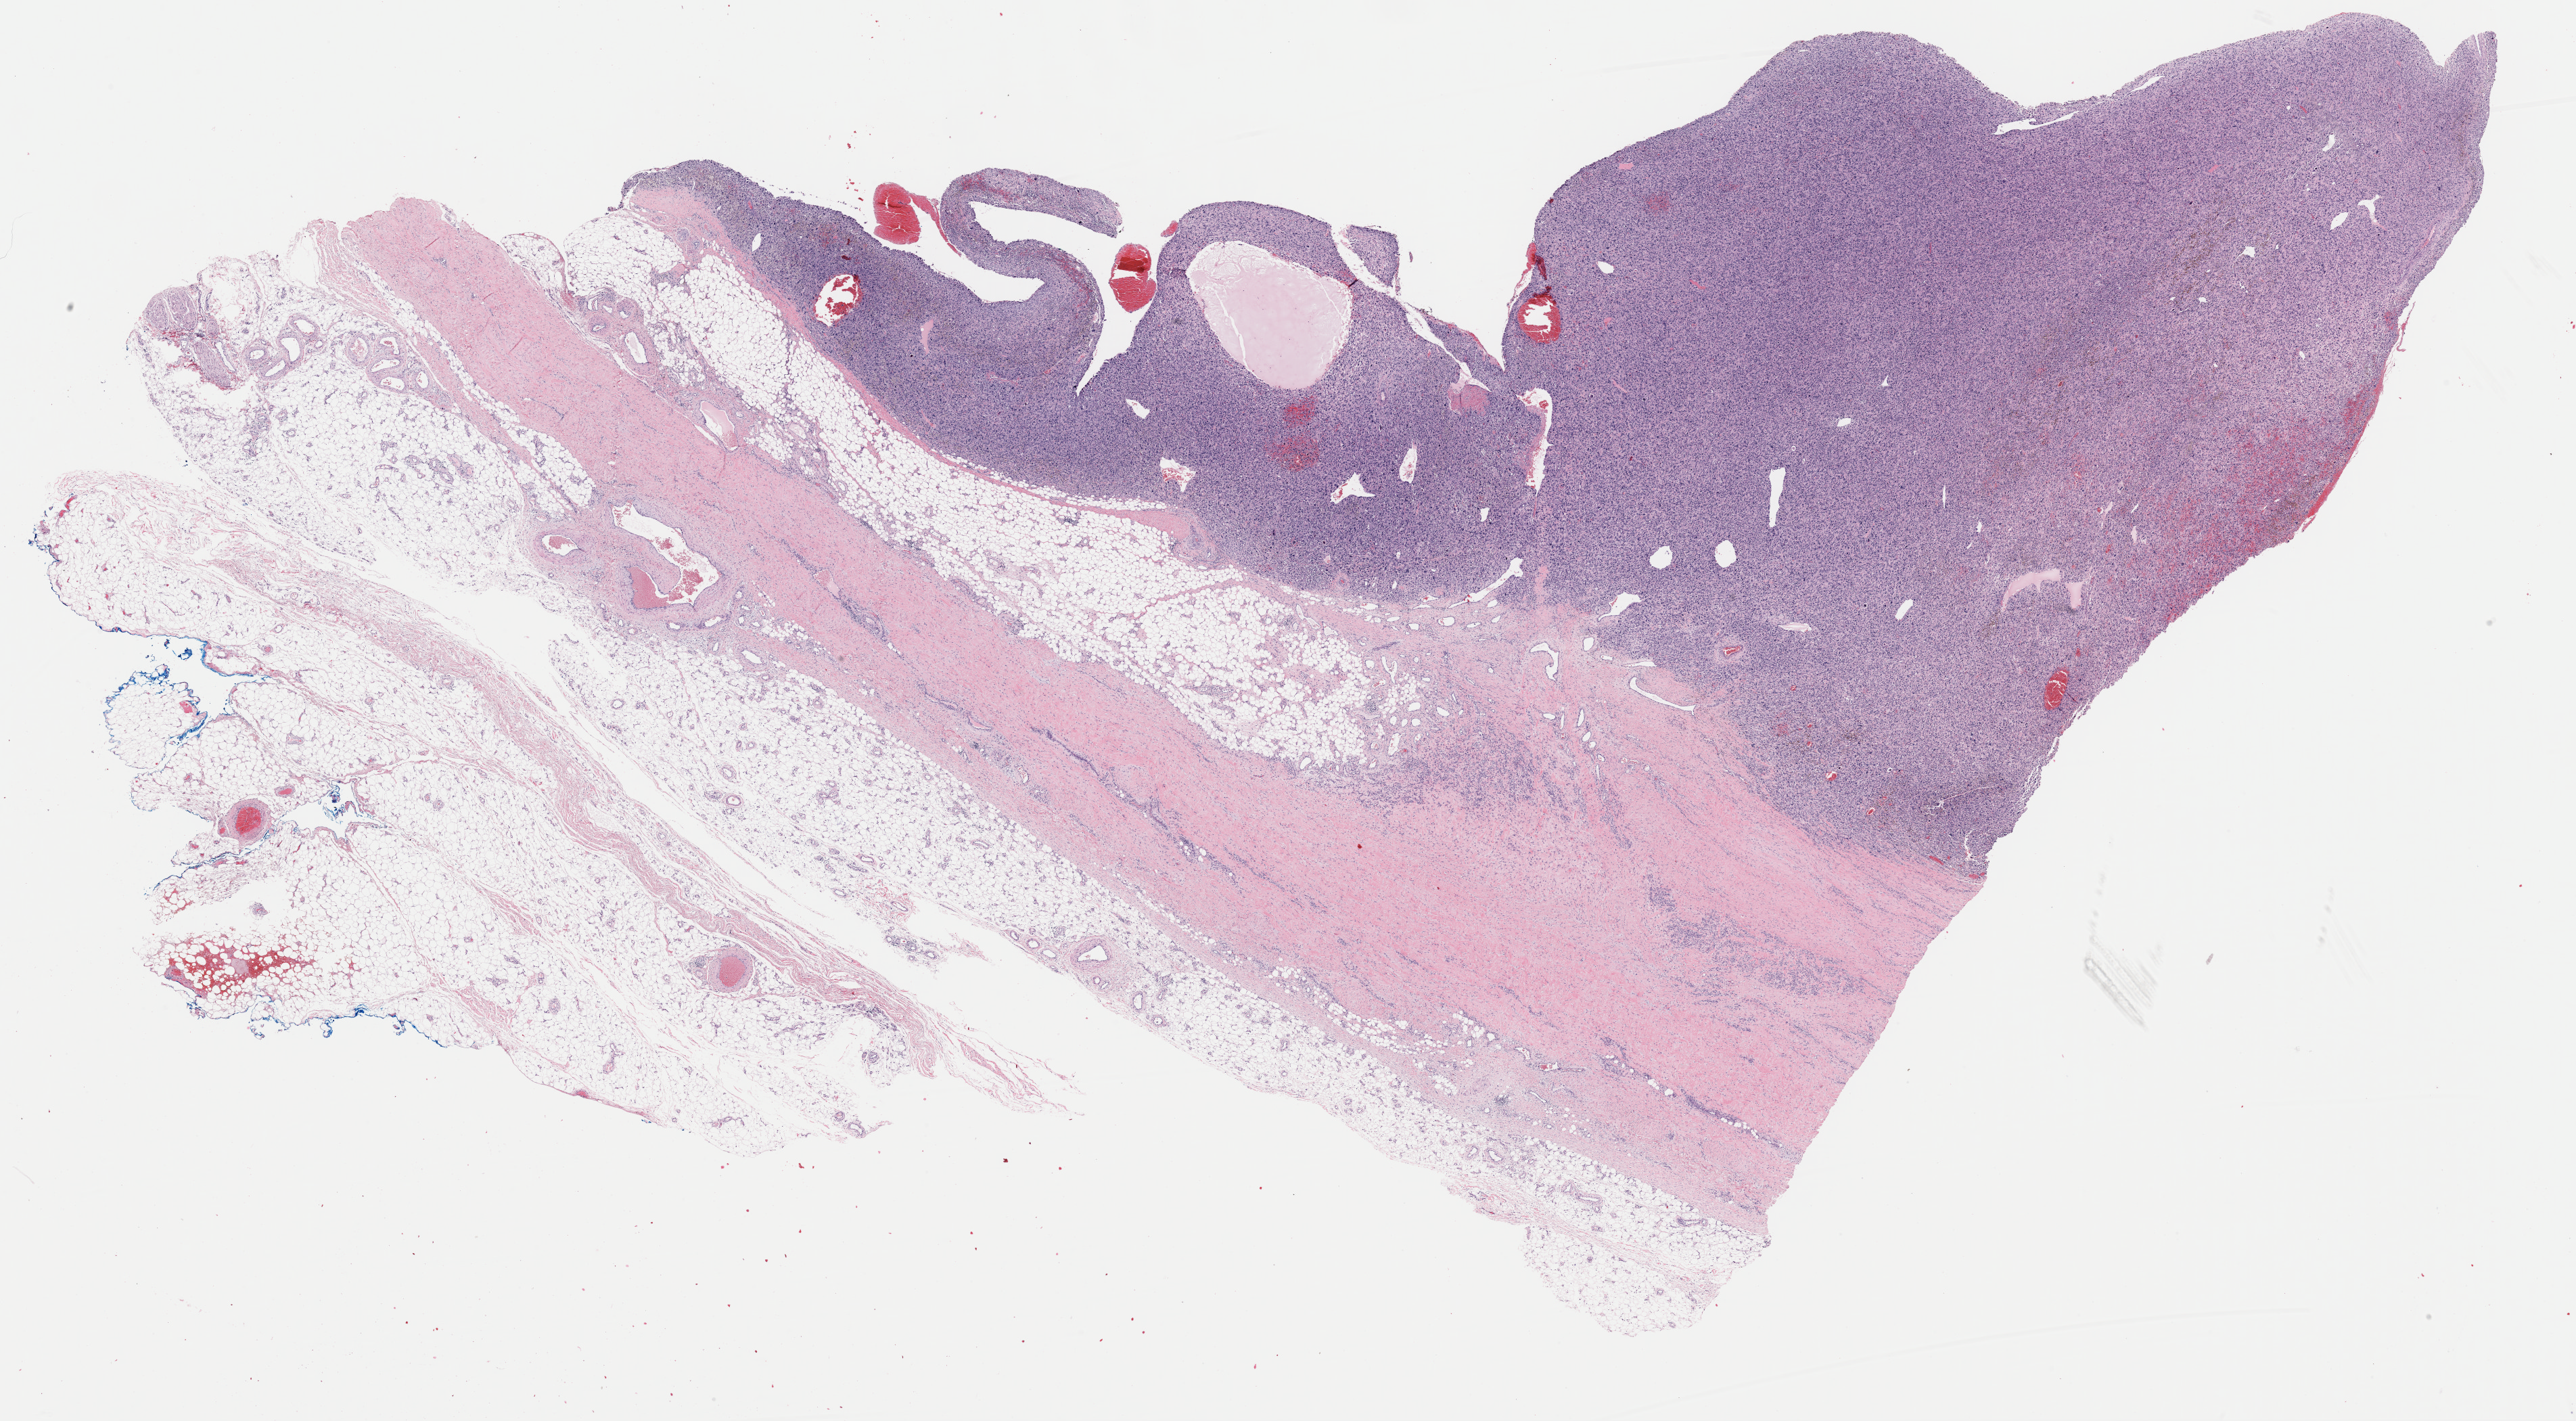
Whole-slide histology image, H&E, whole scanned area (about 30.1 x 16.6 mm, acquisition: 40x scan) shown as a low-resolution overview, formalin-fixed paraffin-embedded (FFPE) diagnostic section, primary tumour sample from the connective, subcutaneous and other soft tissues. Patient: female, age at initial diagnosis 75 years.
Pathologic diagnosis: Malignant fibrous histiocytoma (connective, subcutaneous and other soft tissues of lower limb and hip).